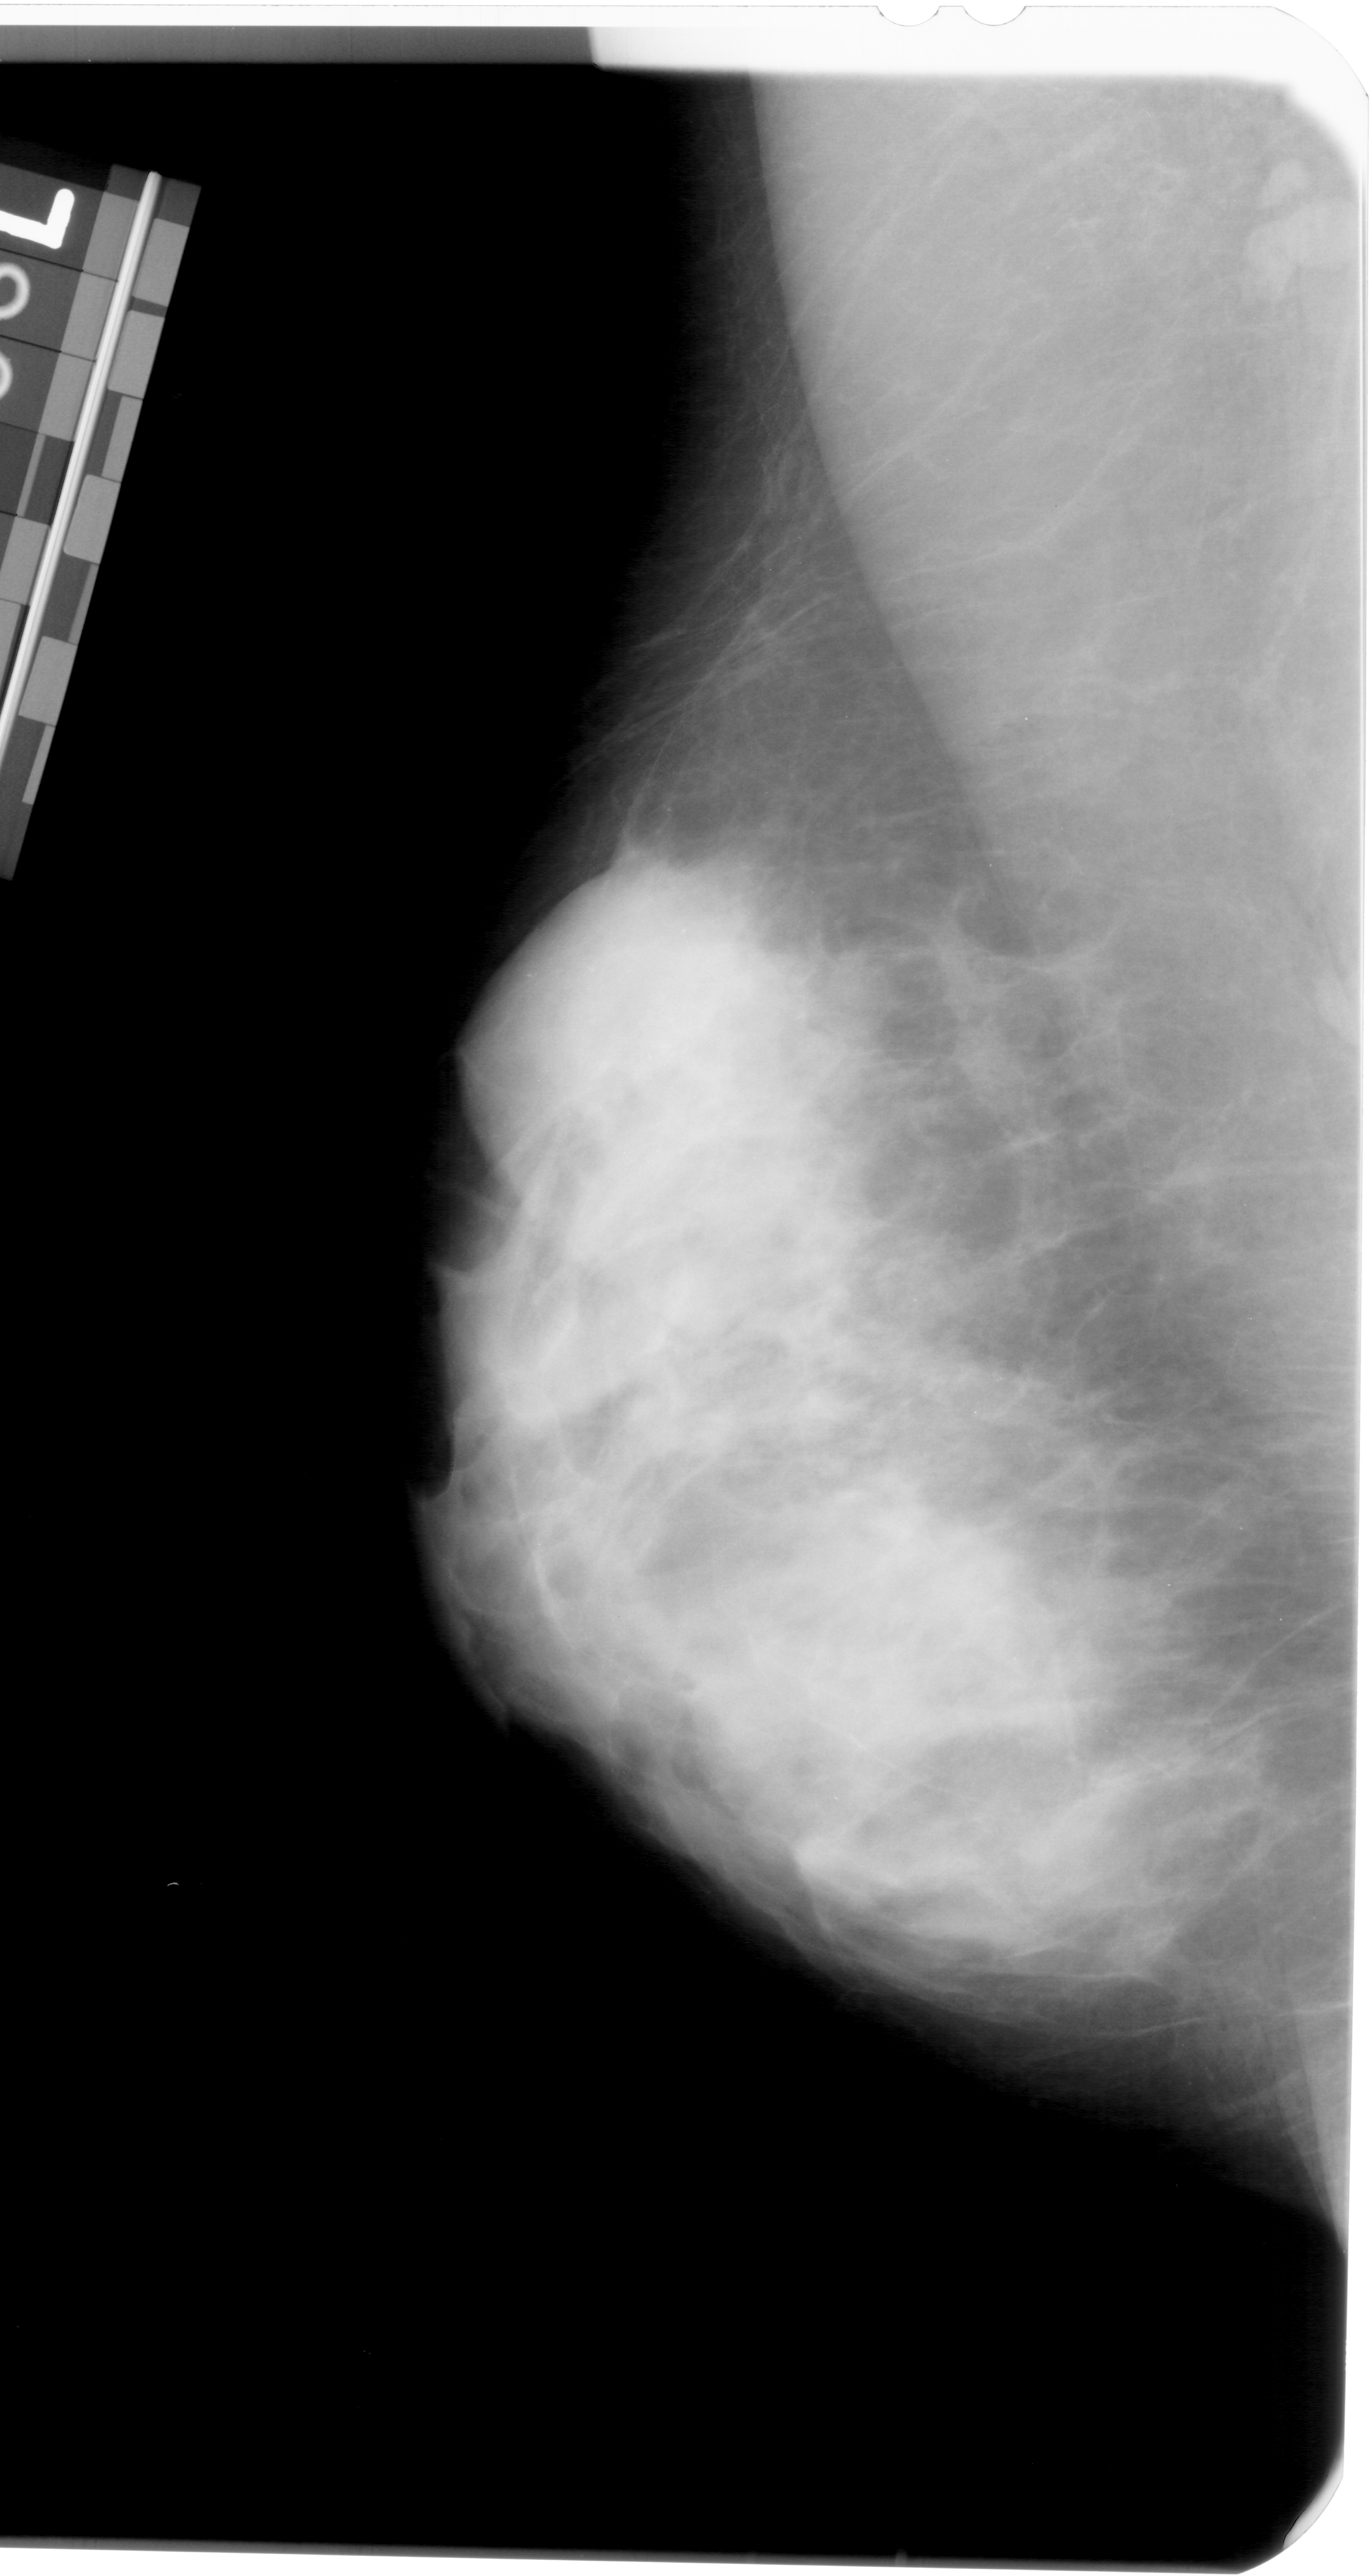
Scanned film-screen mammogram. Left breast. MLO view. 1370 × 2576 image matrix.
Expert-marked regions of interest on this image (one box per marked abnormality):
- calcifications, morphology pleomorphic, distribution segmental; BI-RADS assessment category 4; subtlety rating 2 on a 1 (subtle) to 5 (obvious) scale; pathology (as recorded): benign: bounding box (x1, y1, x2, y2) in pixels: (460, 857, 882, 1297)